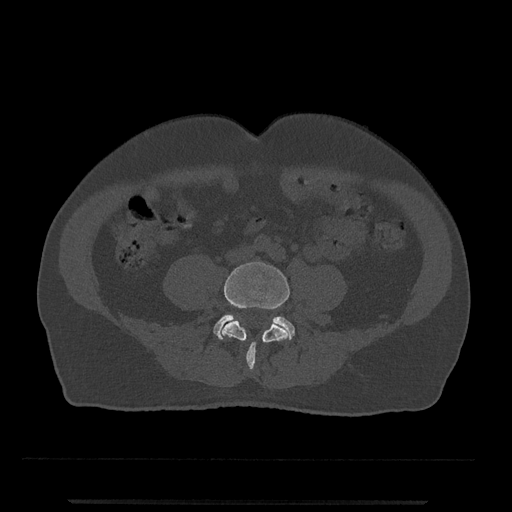
CT including the spine, one axial slice. Slice 113 of 797 in the series (ordered by position). Reconstruction kernel Br40s/3. Bone window (W 1800 / L 400 HU). 0.5 mm slice thickness. 512 × 512 image matrix, field of view 419 × 419 mm. Patient: male, 63 years. Case-level facts recorded for this patient, not image findings: primary cancer: prostate.
Structures marked on this image (semi-automatic segmentation, software-assisted and operator-edited):
- L4 vertebra: box from (x=222, y=262) to (x=290, y=371) px
- L5 vertebra: (x=214, y=314)–(x=295, y=340)